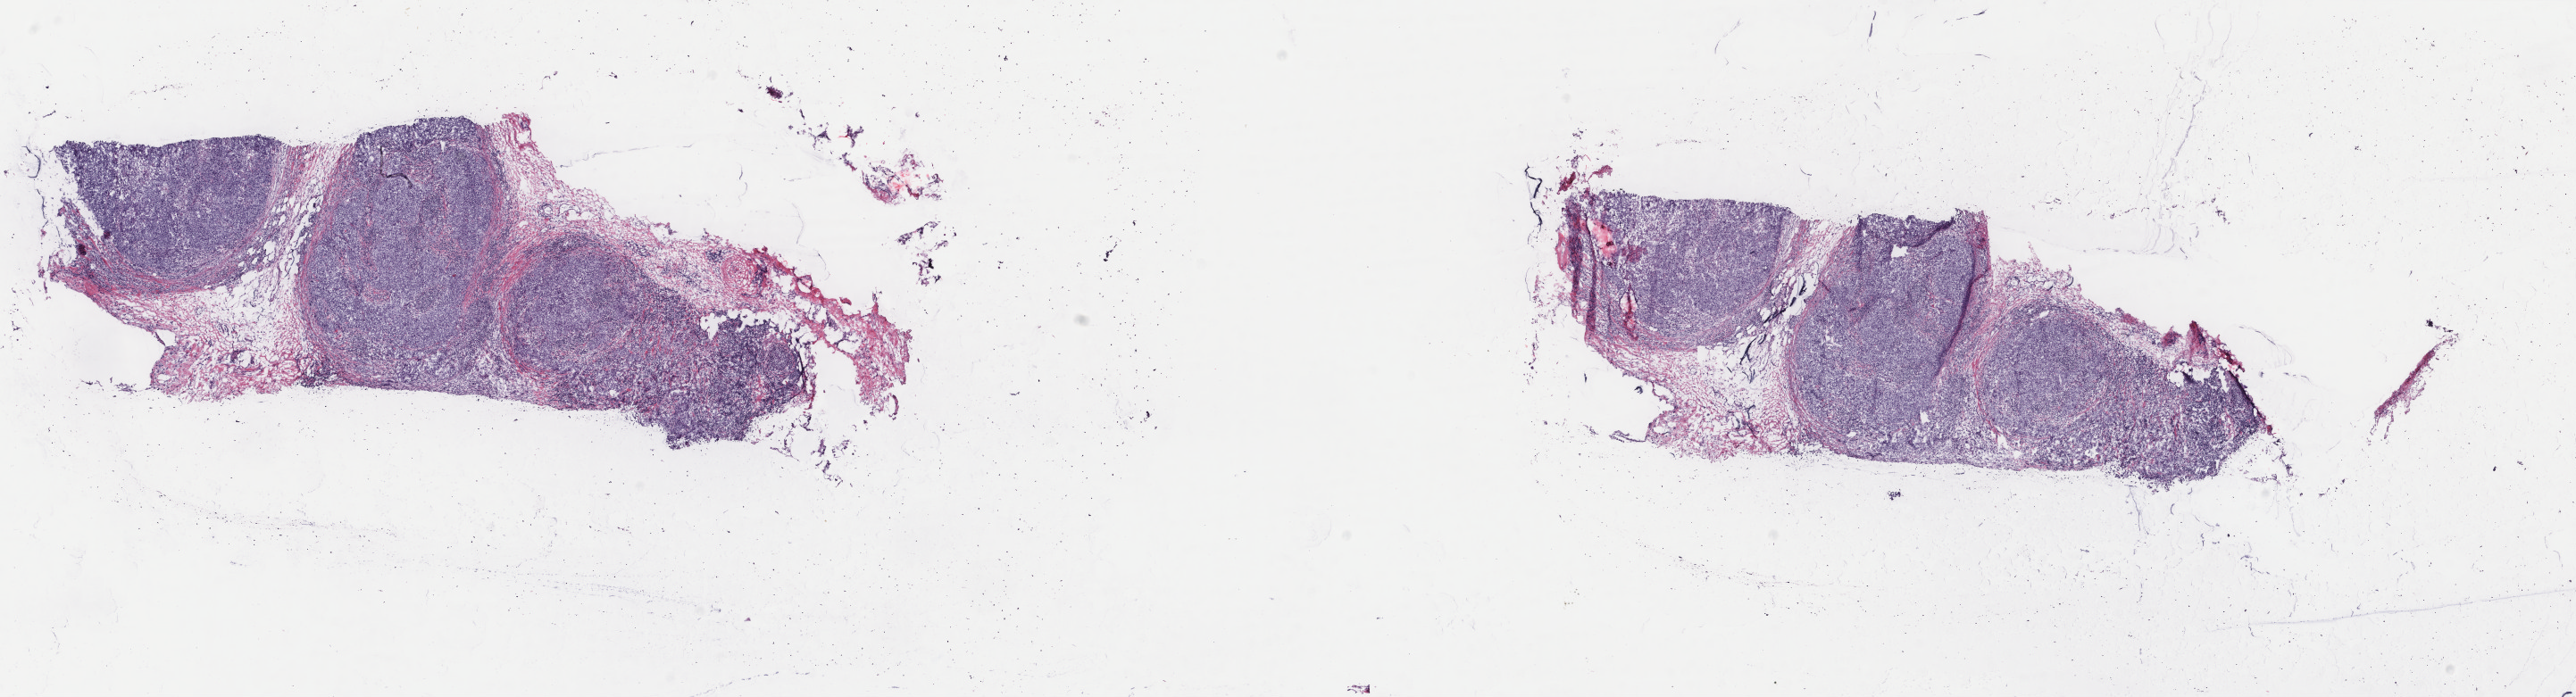
Whole-slide histology image, H&E-stained, shown as a low-resolution overview of the whole scanned area (about 22.9 x 6.2 mm), frozen section from the top of the tissue portion, sample: primary tumour, breast. Female patient. Composition of this section per pathologist review: tumour cells 80%, tumour nuclei 65%, normal cells 0%, stromal cells 20%, necrosis 0%. Infiltration values recorded for this section: lymphocyte infiltration 0%, monocyte infiltration 0%, neutrophil infiltration 0%.
Lymph nodes positive (case pathology): 0 of 8 examined. Pathologic diagnosis: Infiltrating duct carcinoma, NOS. AJCC pathologic stage: I (6th edition). Laterality: right.